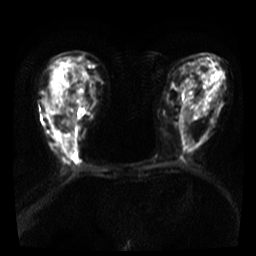
Breast MRI, one axial slice. Slice 14 of 36 in the series (ordered by position). Diffusion-weighted series; image 2 of 4 stored at this slice position (different b-values; order by instance number). 3 T. 256 × 256 image matrix, field of view 300 × 300 mm. Female patient.
Annotated regions visible in this slice (expert manual segmentation):
- tumour on diffusion-weighted imaging: box from (x=62, y=143) to (x=73, y=155) px